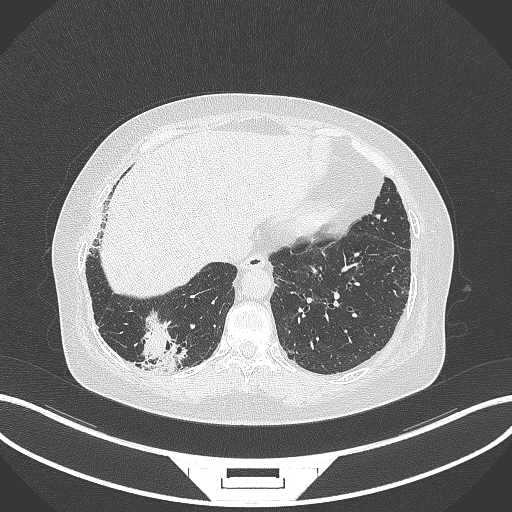
Chest CT, one axial slice. Slice 36 of 296 in the series (ordered by position). 120 kVp. Lung window (W 1500 / L -600 HU). 512 × 512 image matrix. Patient: female, 65 years. From the clinical record (not read from this slice): clinical TNM (as recorded): T2b N1 M0.
Structures marked on this image (bounding box drawn by a radiologist):
- lung tumour (recorded histology: adenocarcinoma): box from (x=137, y=310) to (x=189, y=374) px